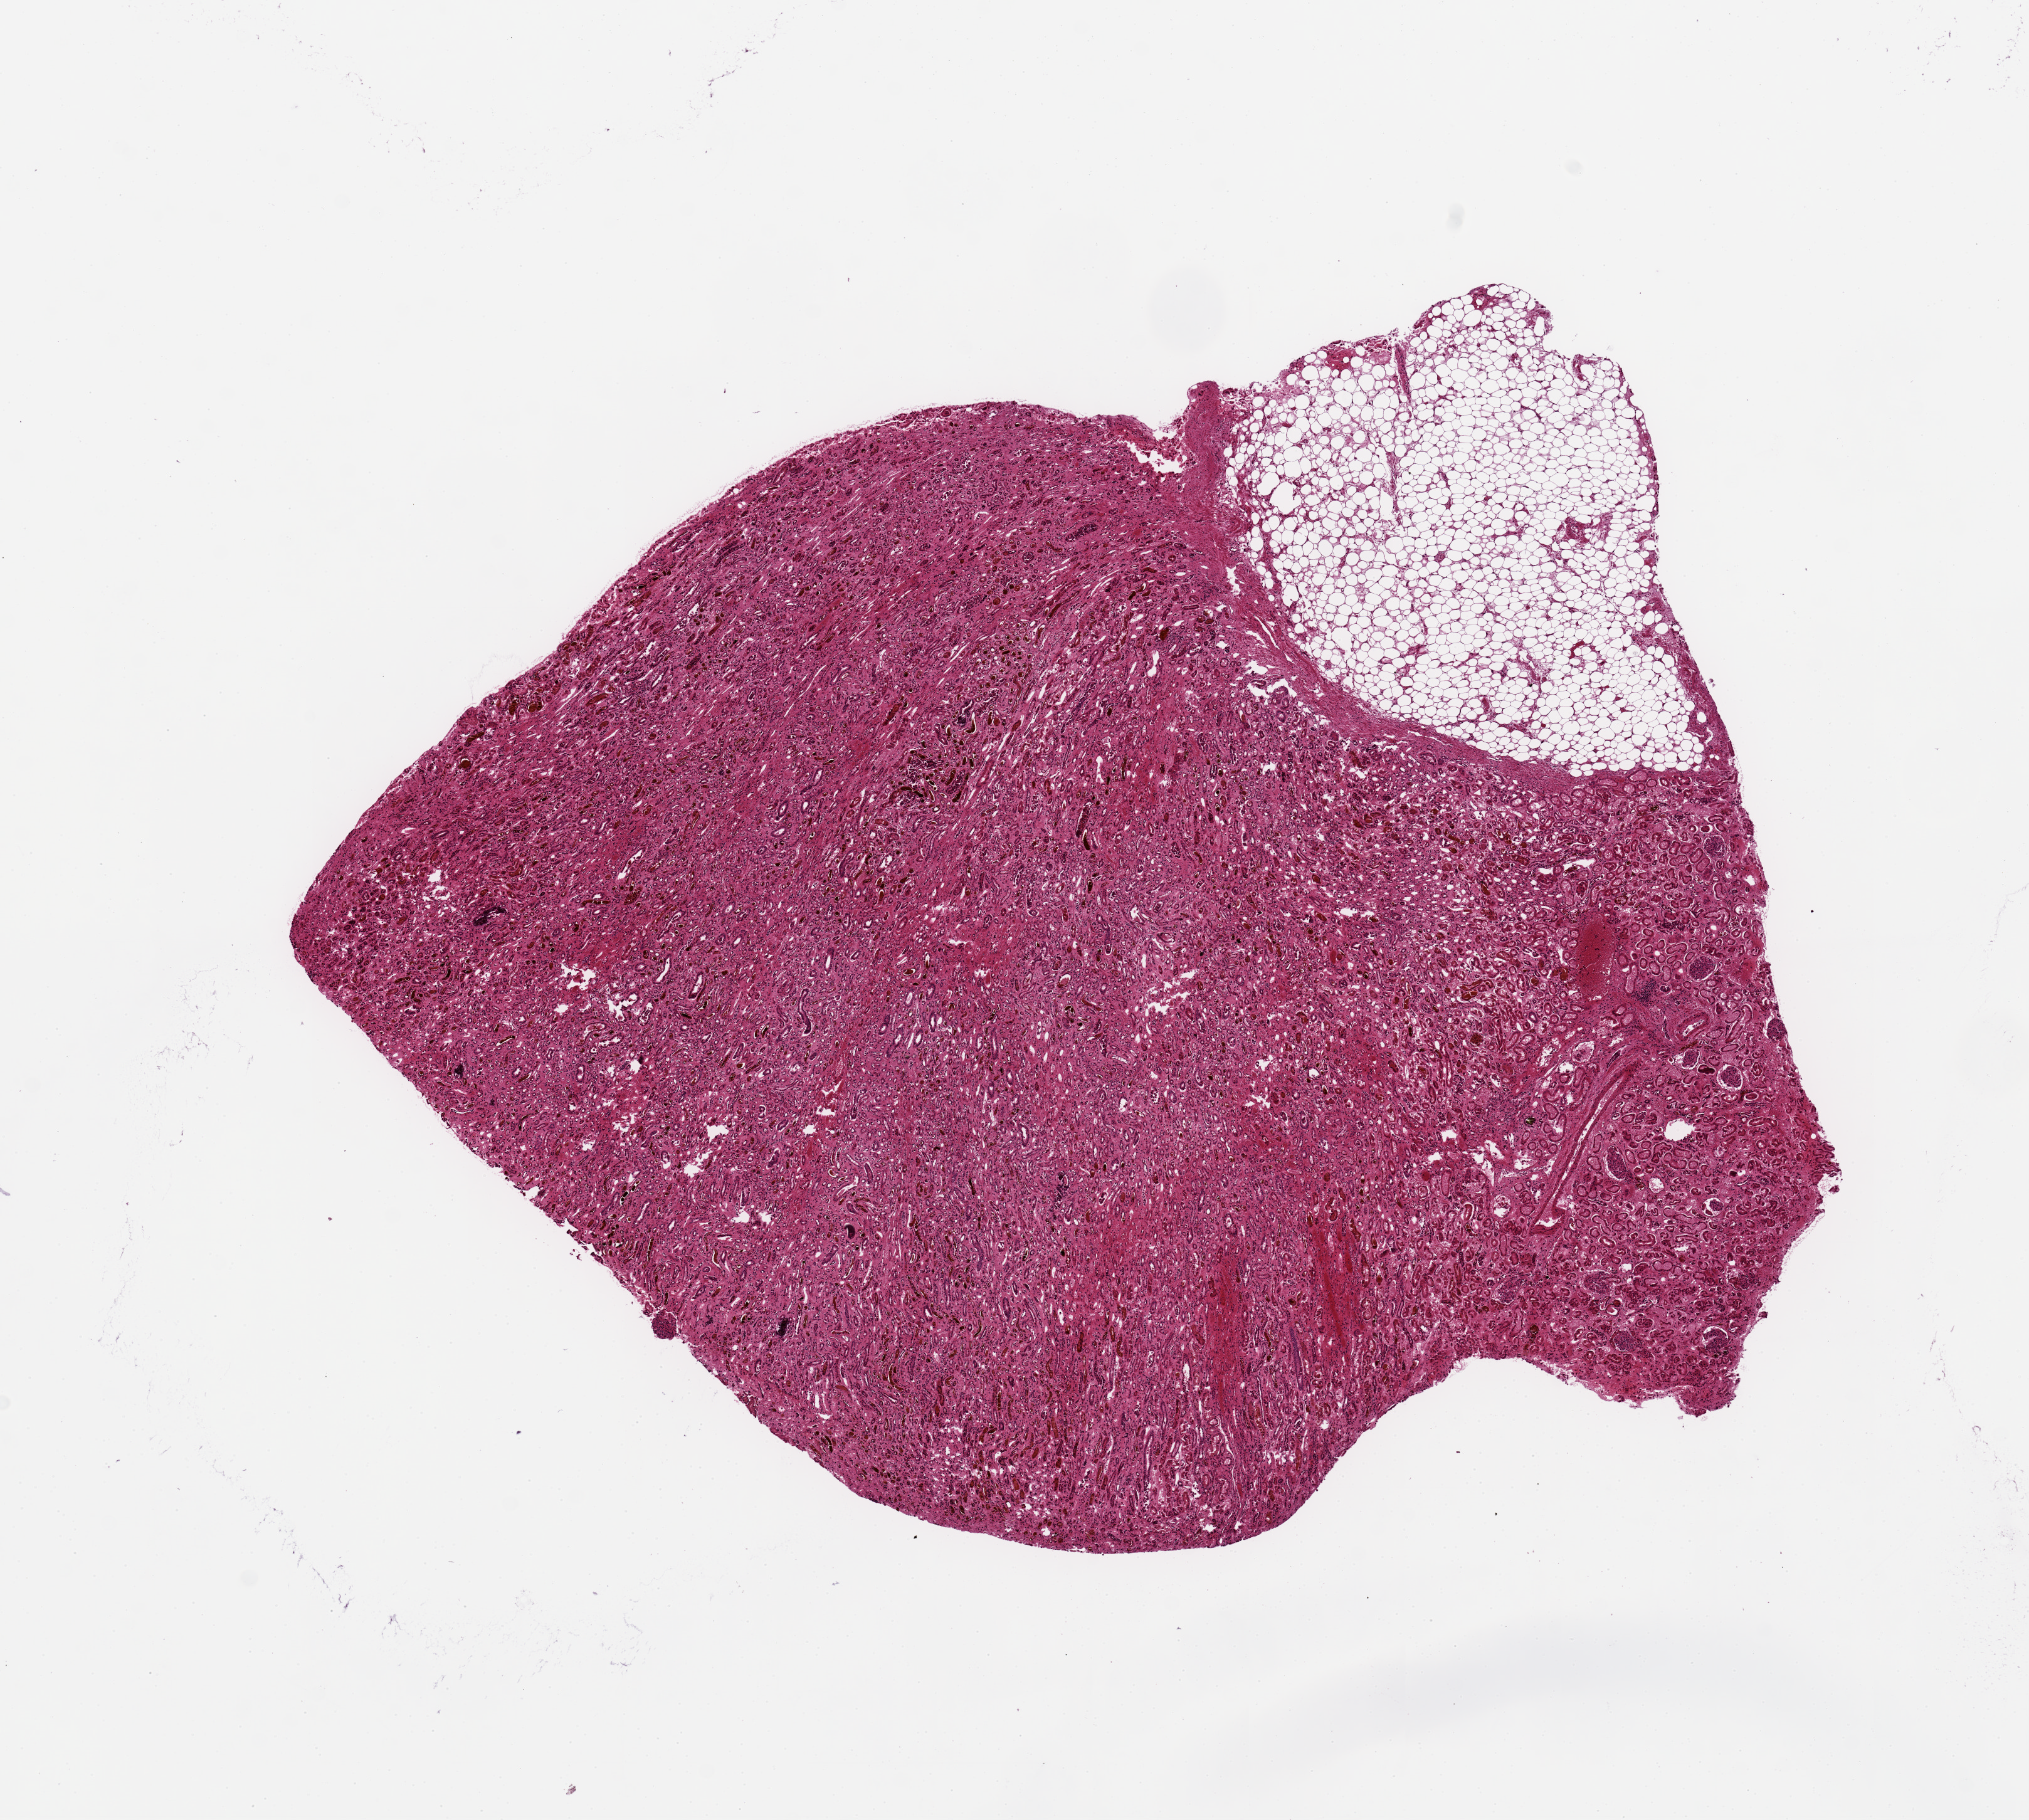
Digitized haematoxylin and eosin-stained section — shown as a low-resolution overview of the whole scanned area (about 12.8 x 11.5 mm, from a 20x scan), PAXgene-fixed, paraffin-embedded tissue, target tissue: renal medulla, donor tissue sample. Male donor.
Review note (as recorded): 9x8.5mm. No glomuruli. Many red cell casts noted.